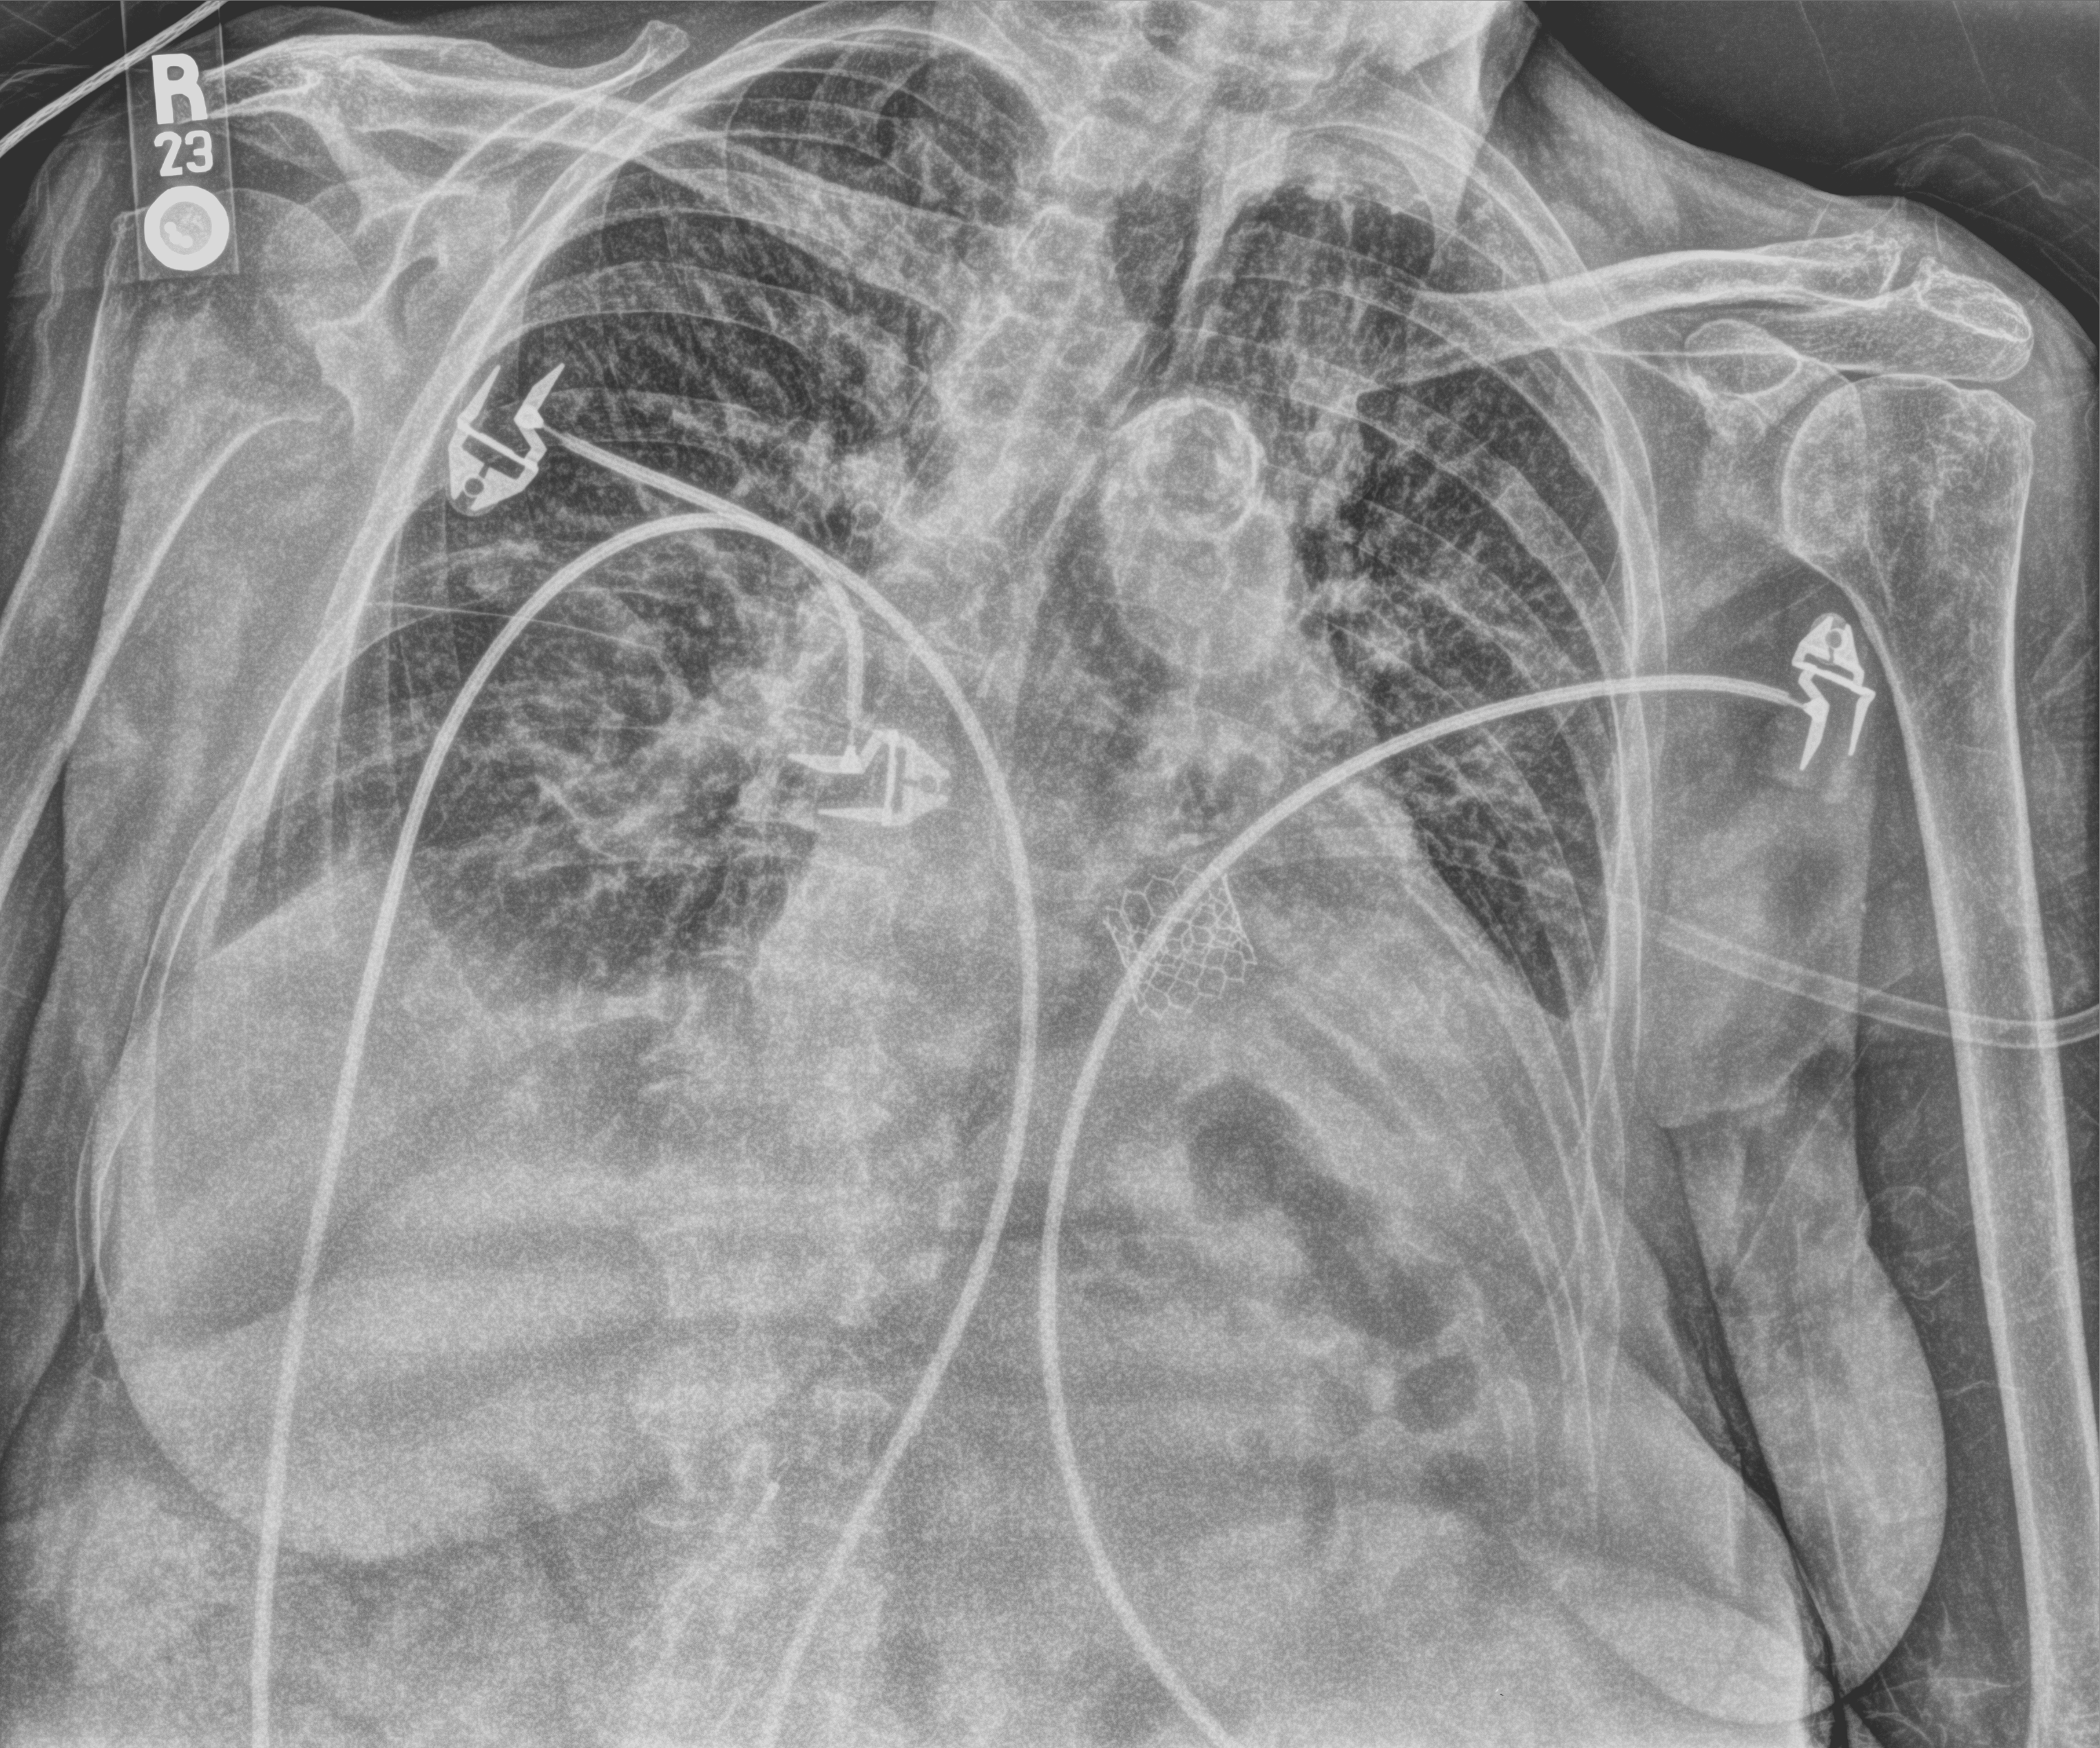
Chest X-ray (portable); anteroposterior (AP) projection. Female patient hospitalised with COVID-19, age 75–90 years.
Hospital-stay facts (about this admission, not read from this image; timing relative to this image not recorded): mechanically ventilated during this hospital stay: no; hypertension (admission record): yes.